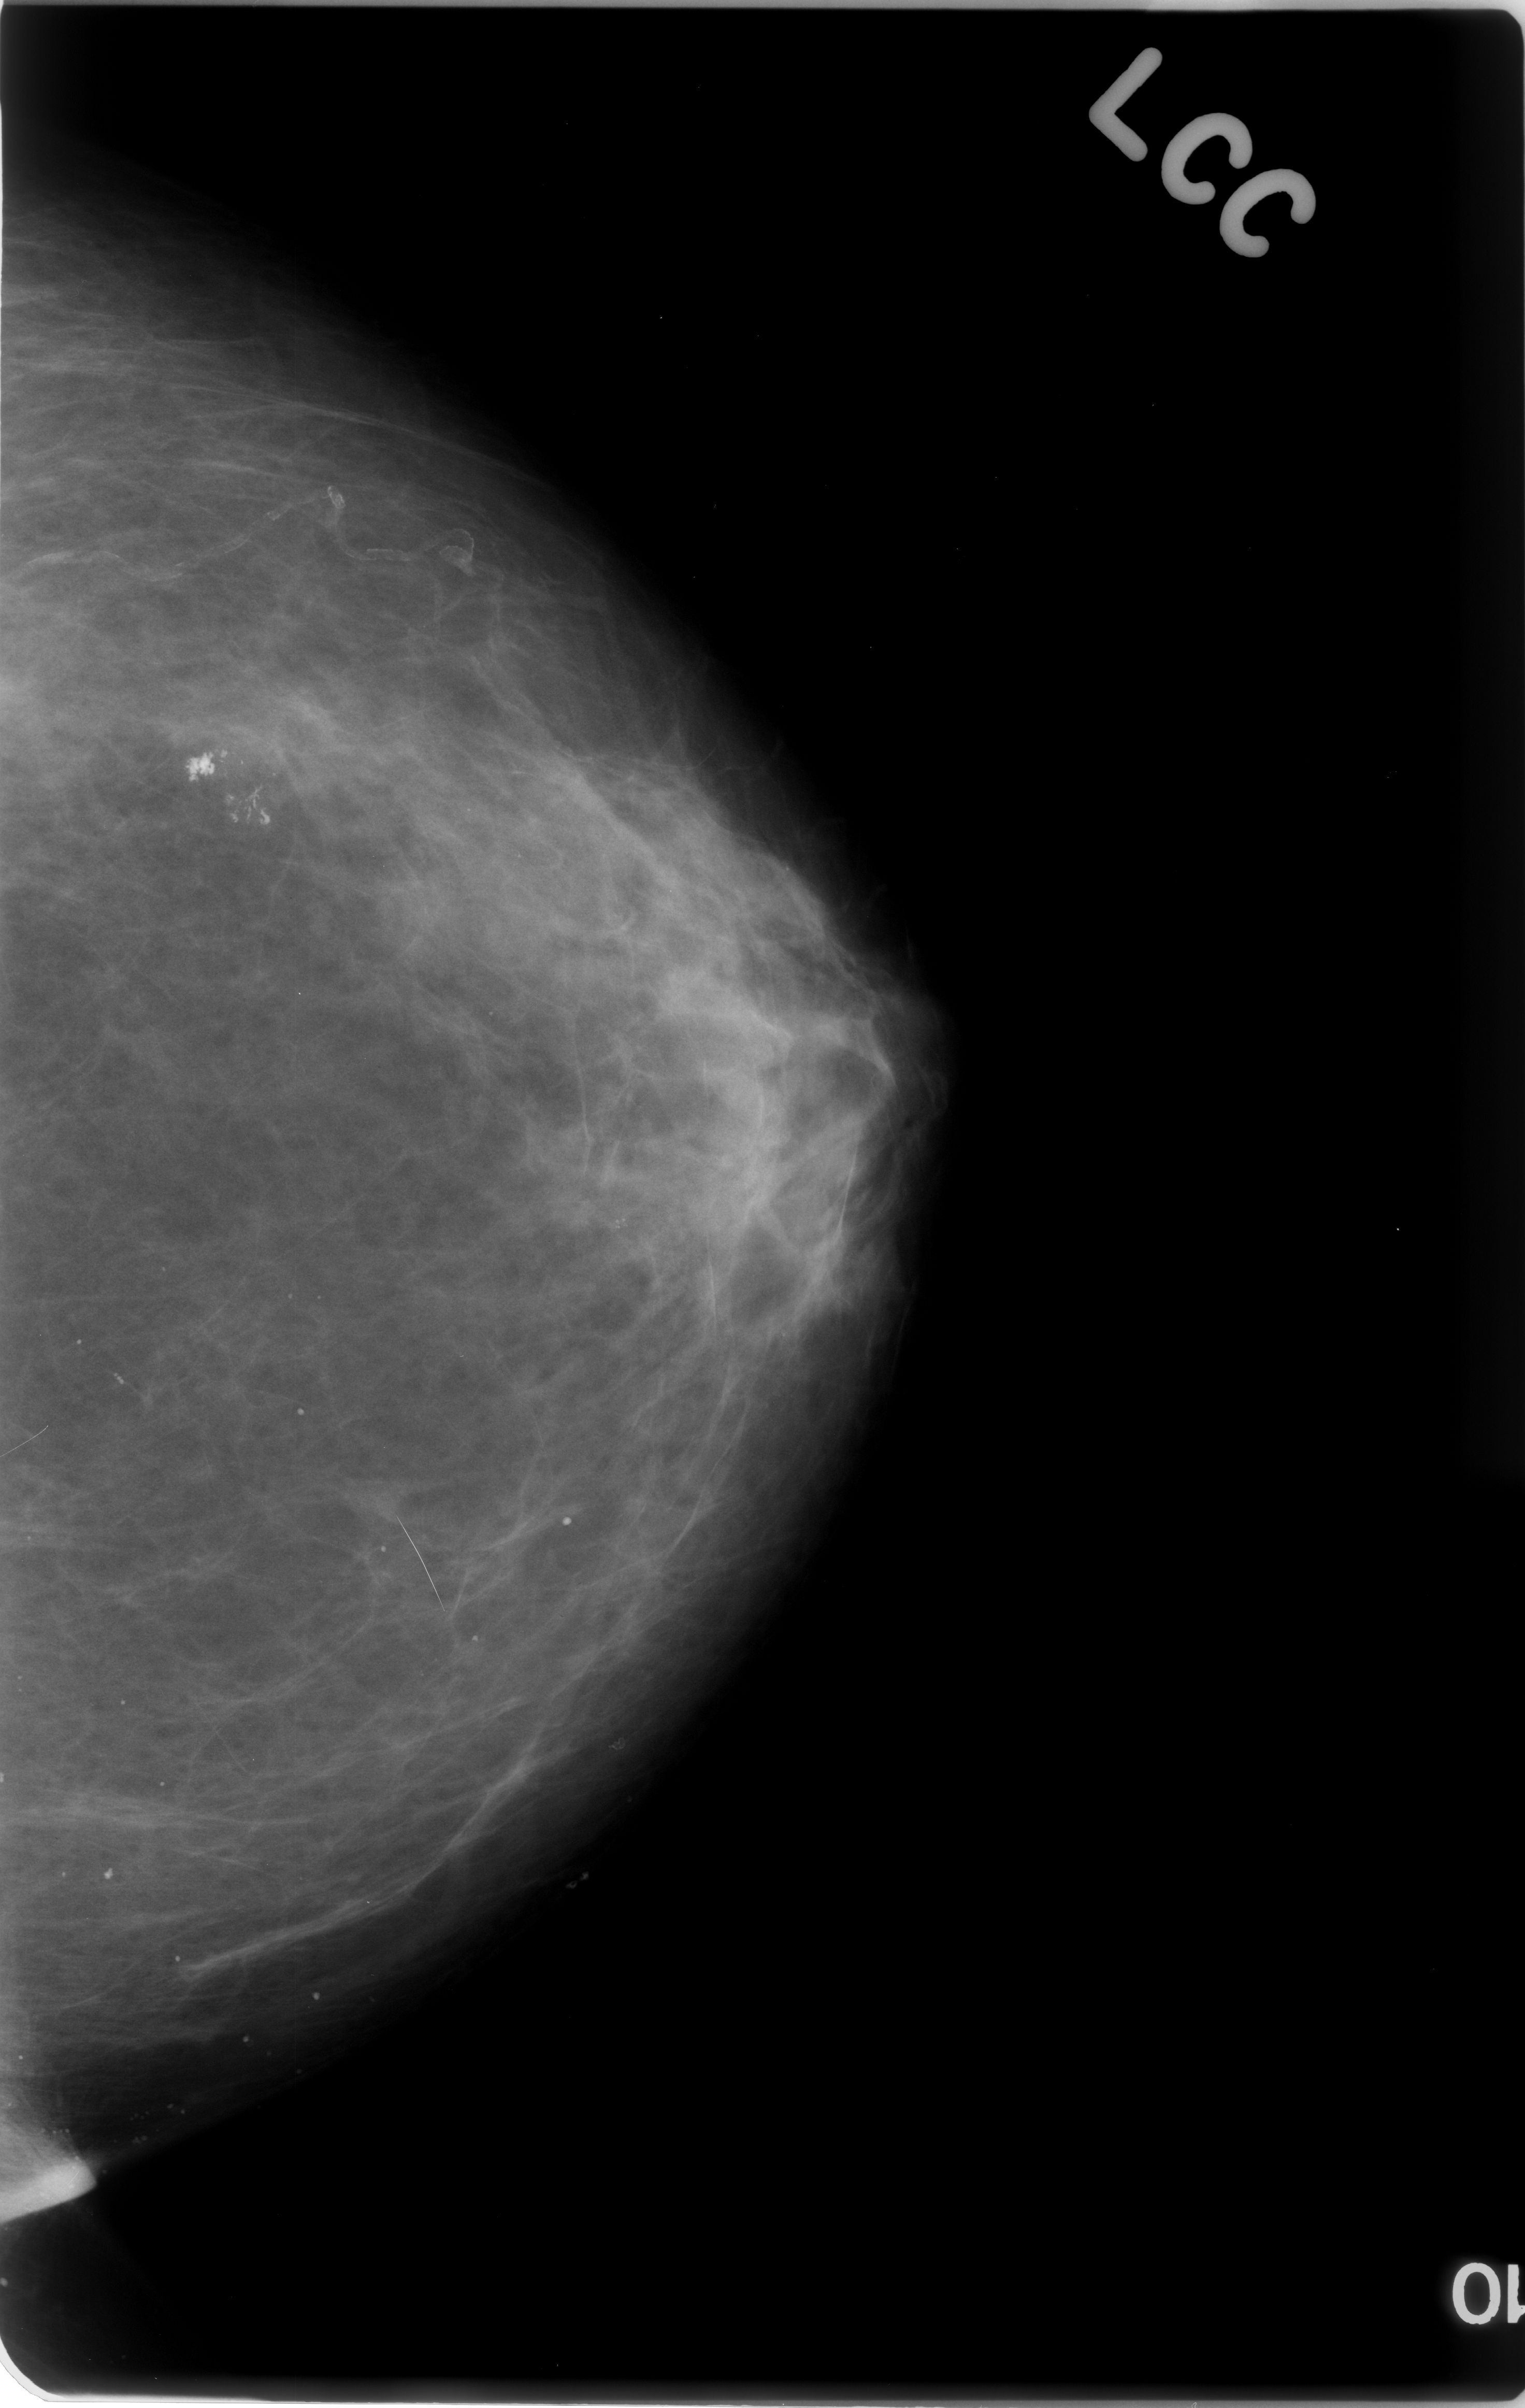
Digitized screen-film mammogram, left breast, CC view, BI-RADS breast density category 1 (scale 1–4).
Calcifications, morphology pleomorphic / fine linear branching, distribution clustered; BI-RADS assessment category 3; pathology (as recorded): benign.